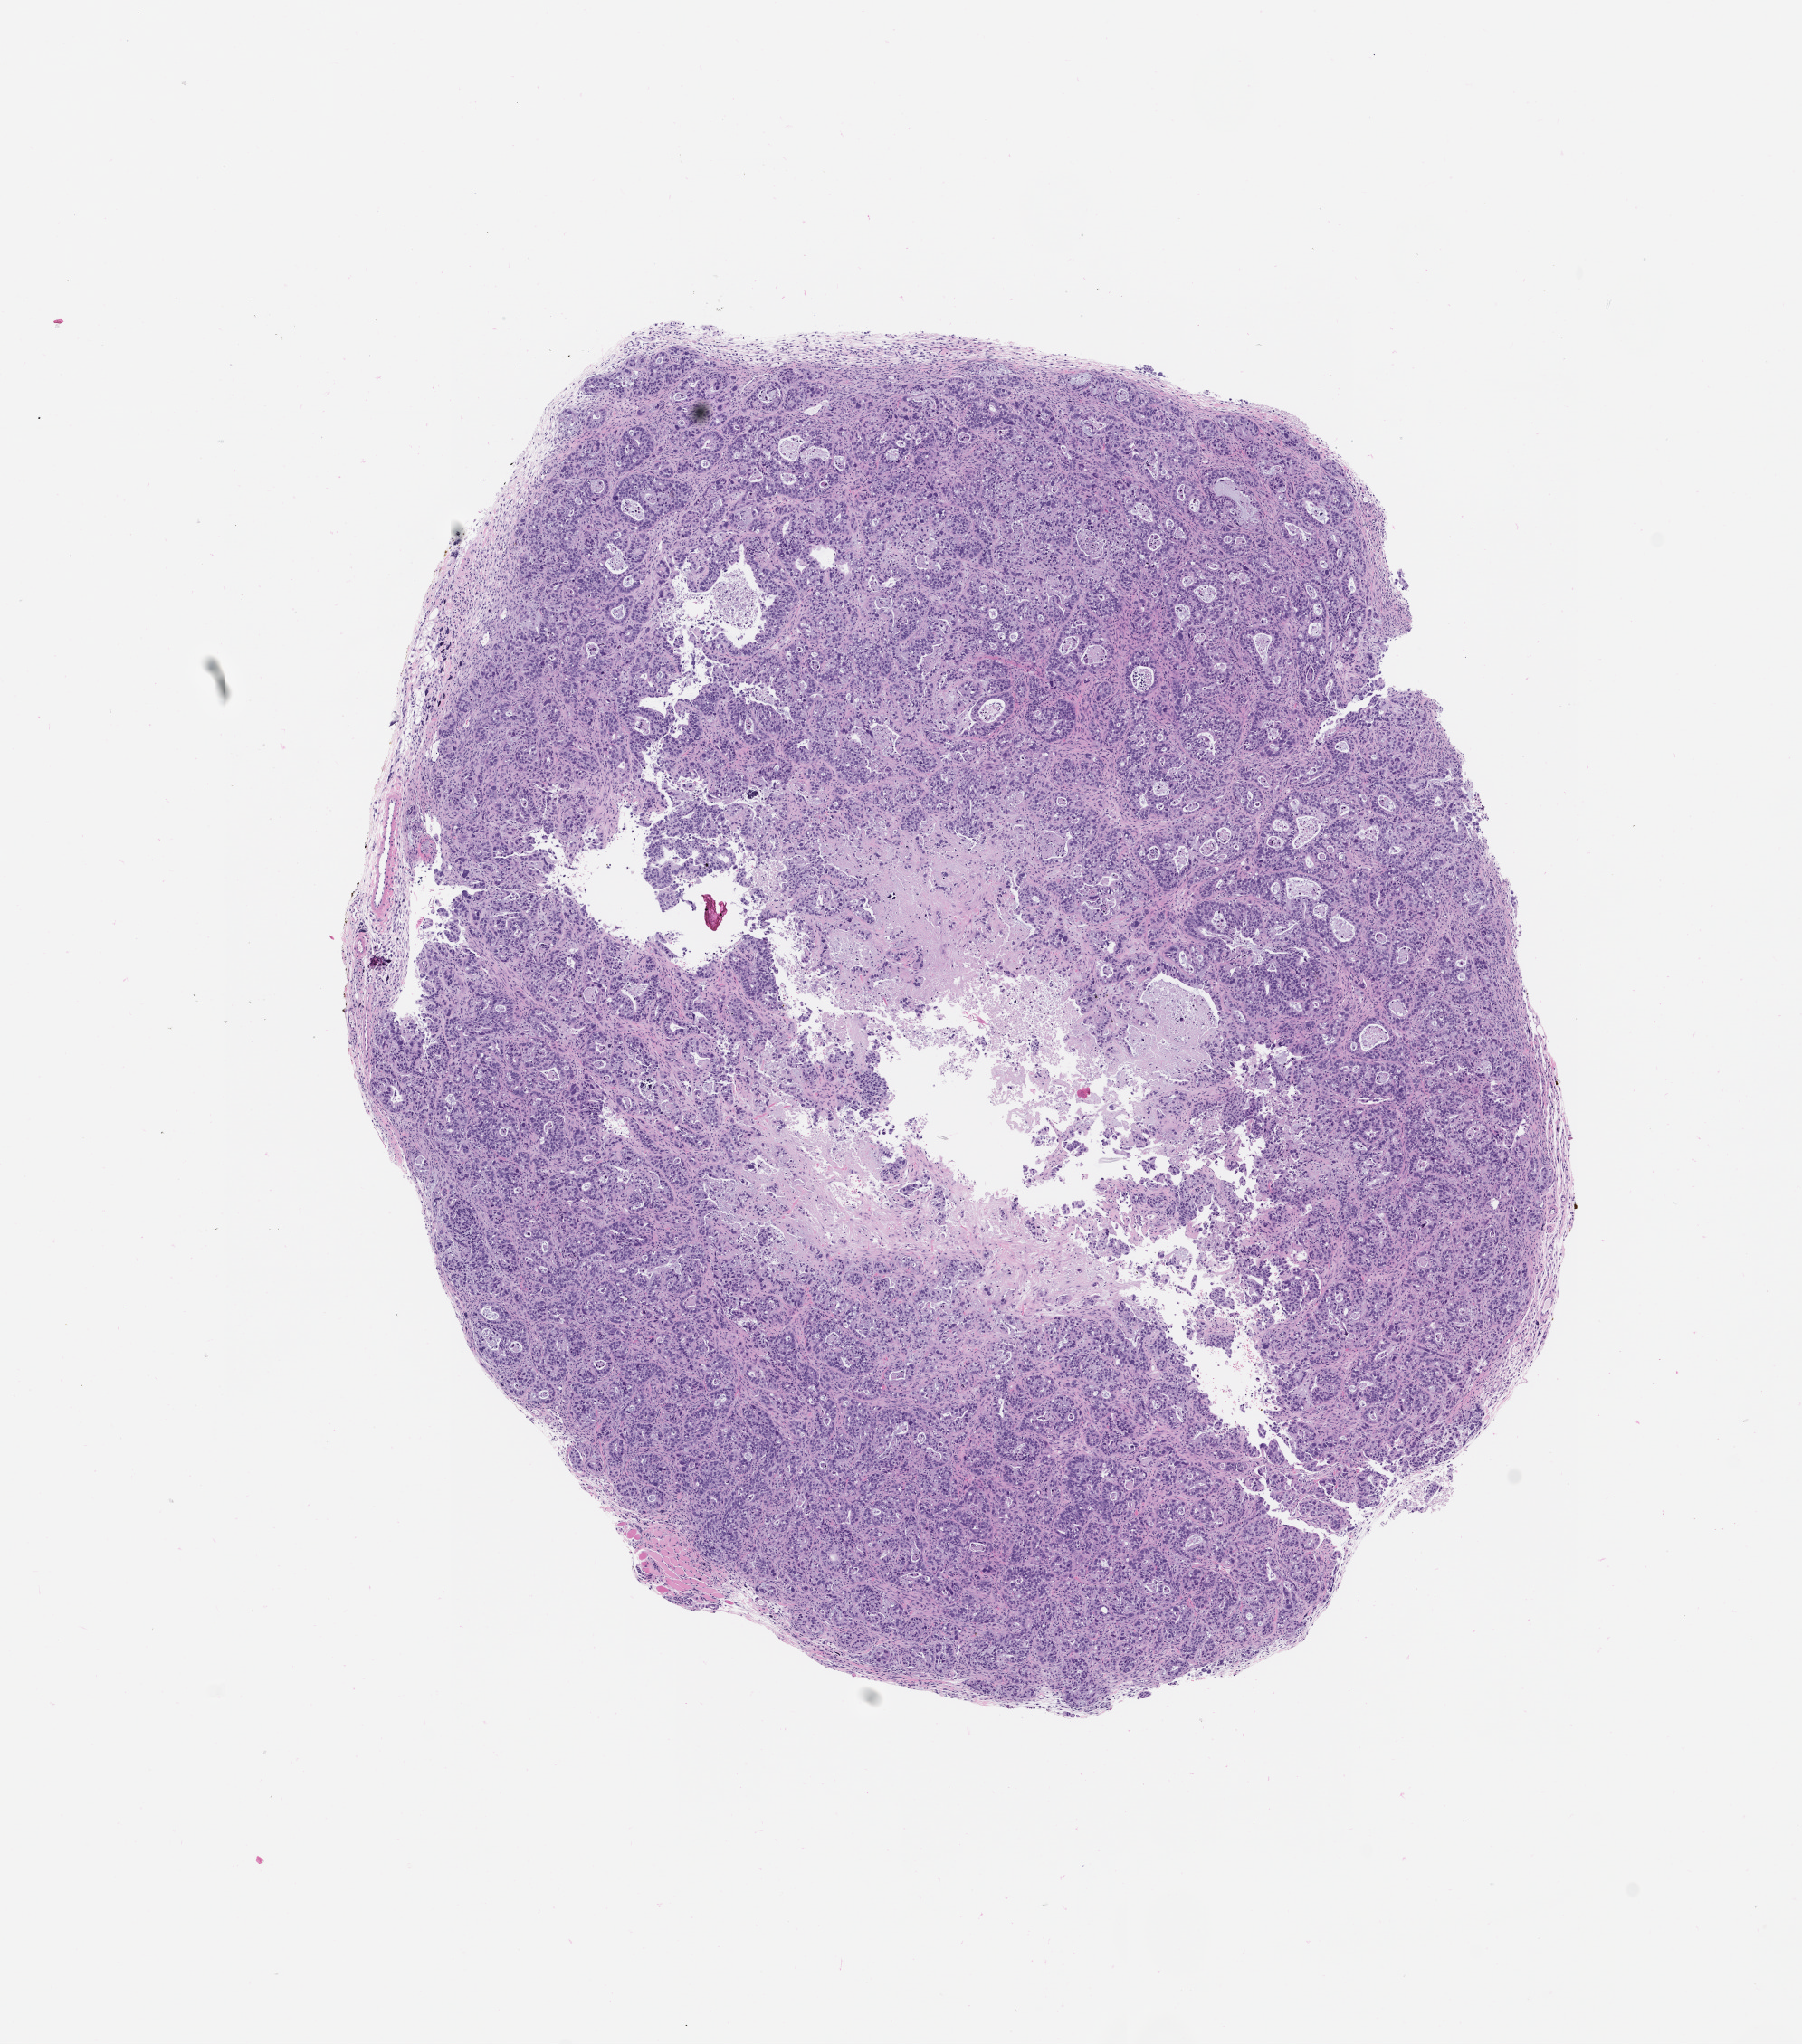
Whole-slide image, H&E: patient-derived xenograft (human tumor grown in a mouse), passage 0, a low-resolution overview of the entire scanned area, about 8.0 x 9.1 mm, formalin-fixed, paraffin-embedded (FFPE) tissue, tumor site category: pancreas.
- originating patient diagnosis: Pancreatic Adenocarcinoma